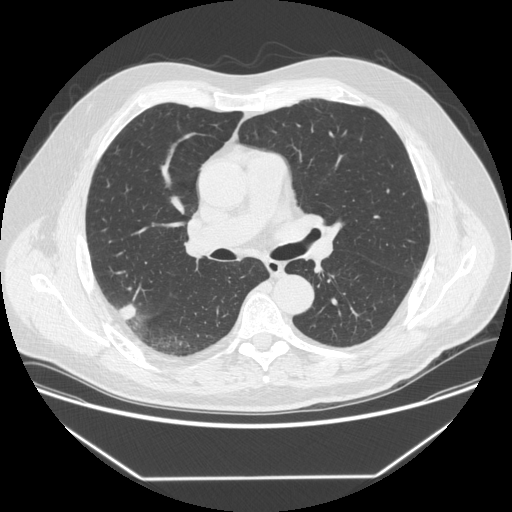
Low-dose screening chest CT, one axial slice. Slice 211 of 342 in the series (ordered by position). Reconstruction kernel STANDARD. Lung window (W 1500 / L -600 HU). 1.25 mm slice thickness. 512 × 512 image matrix, field of view 410 × 410 mm.
Annotated regions visible in this slice (outlined manually by an expert reader):
- lesion 1 (tumor, upper lobe of right lung): box from (x=119, y=303) to (x=137, y=320) px